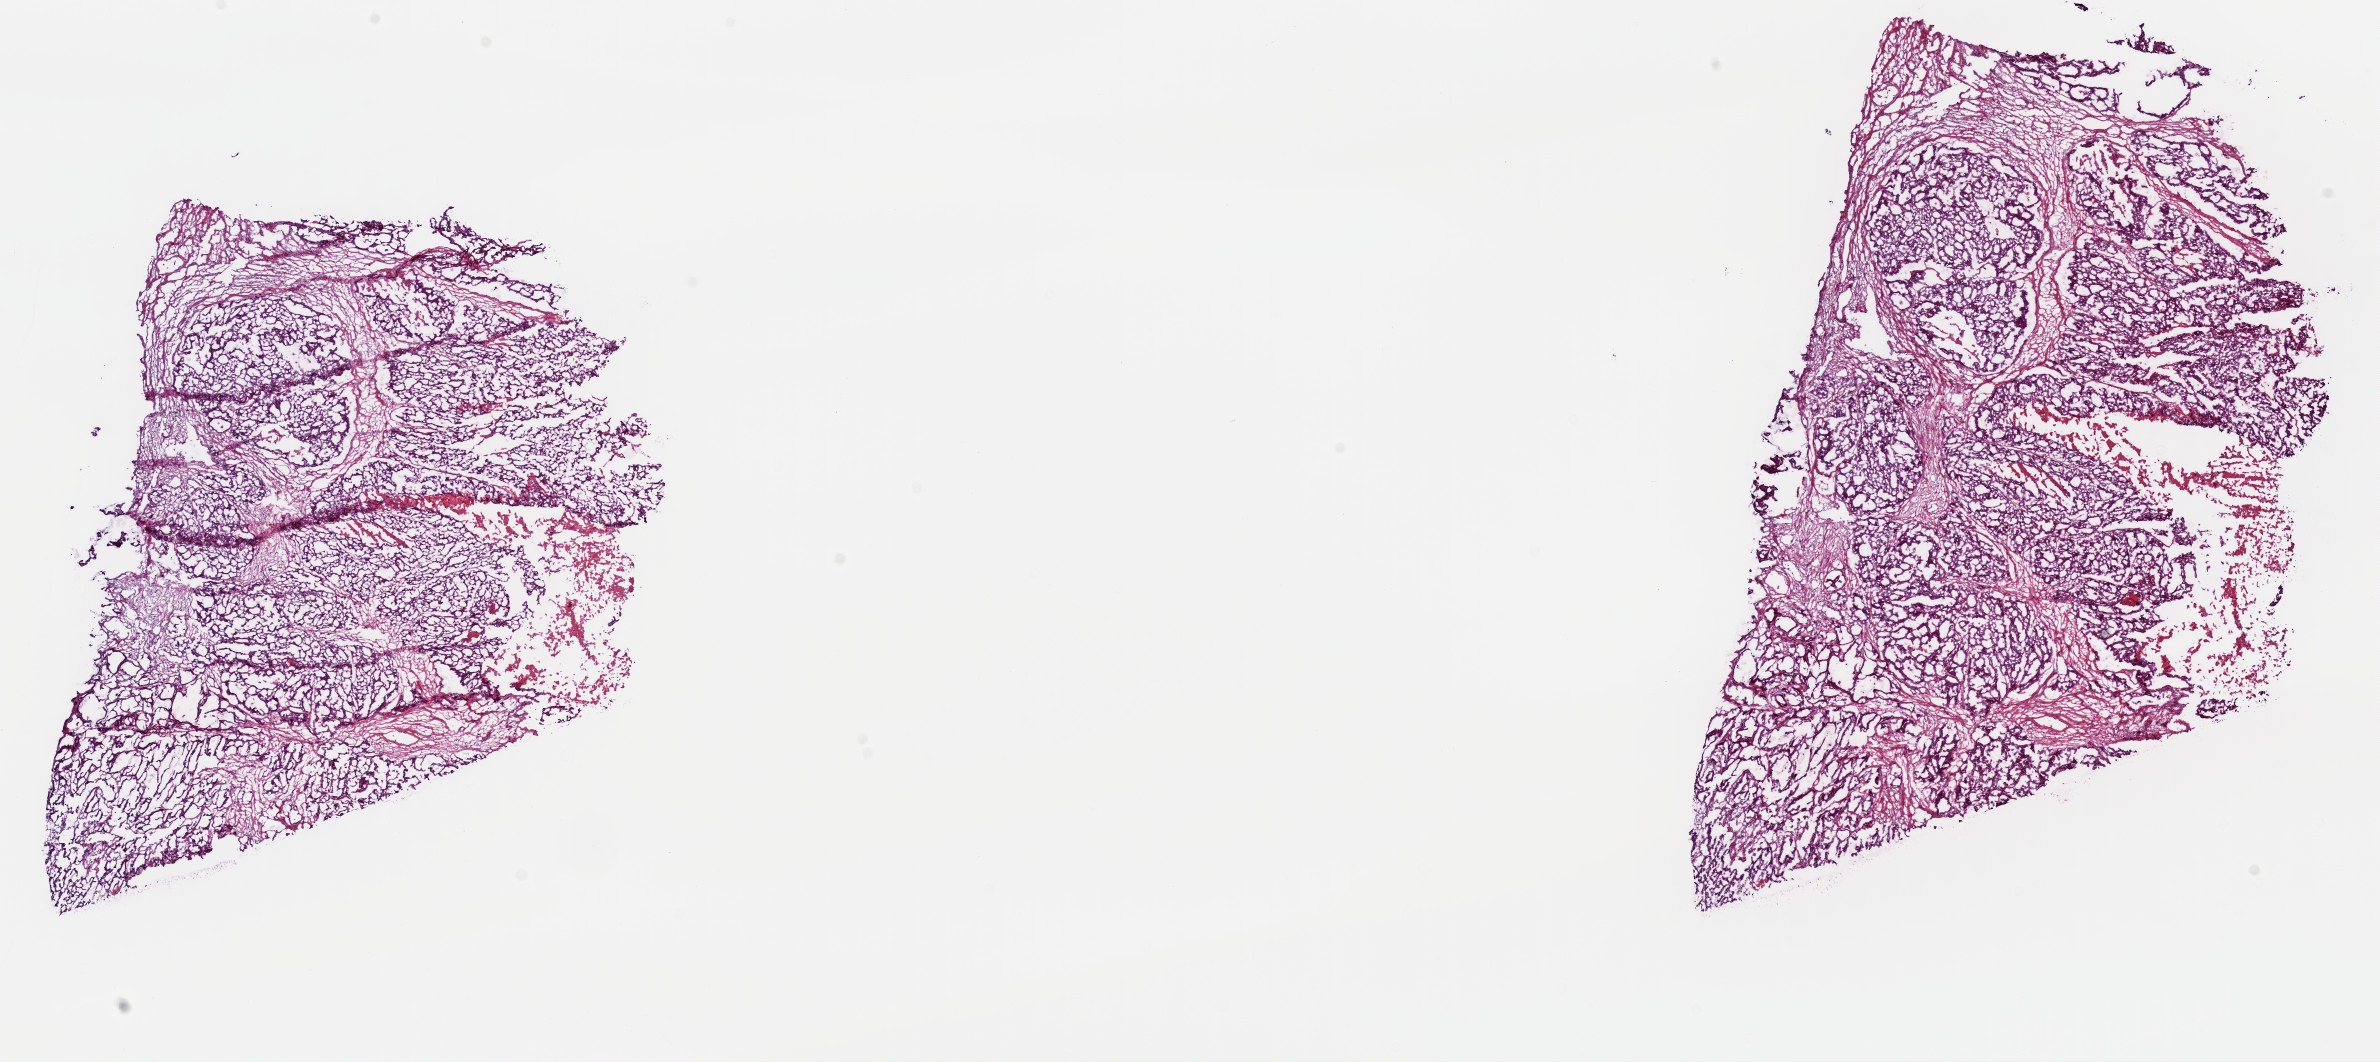
H&E whole-slide image, shown as a low-resolution overview of the whole scanned area (about 18.8 x 8.4 mm, acquisition: 40x scan), frozen section, primary tumour sample from the colon. Female, age 71 years at initial diagnosis. Slide review estimates, as recorded: tumour cells 52%, tumour nuclei 80%, normal cells 0%, stromal cells 30%, necrosis 18%. Inflammatory infiltration, as recorded: lymphocyte infiltration 1%, monocyte infiltration 0%, neutrophil infiltration 0%.
- diagnosis: Mucinous adenocarcinoma (ascending colon)
- AJCC pathologic stage: IV (6th edition)
- TNM: T3 N2 M1